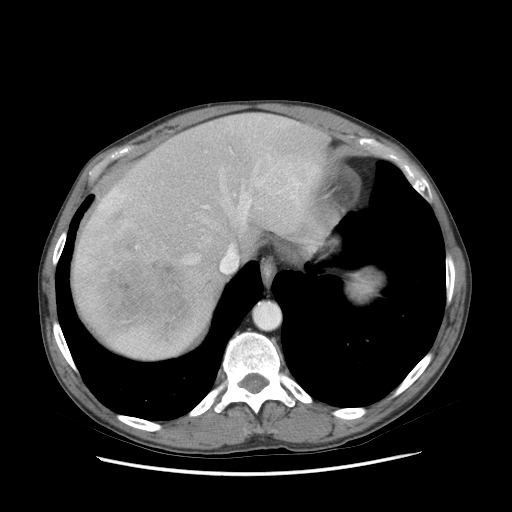
Contrast-enhanced abdominal CT (liver protocol), one axial slice; slice 65 of 89 in the series (ordered by position); reconstruction kernel STANDARD; 140 kVp; soft-tissue window (W 400 / L 40 HU); 2.5 mm slice thickness; 512 × 512 image matrix, field of view 380 × 380 mm. Case-level facts recorded for this patient, not image findings: diagnosis: hepatocellular carcinoma (patient treated with transarterial chemoembolisation; whether this scan precedes or follows treatment is not stated here); TNM stage (as recorded): Stage-IIIB; Child-Pugh class: A; tumour differentiation: moderately differentiated; tumour nodularity: multinodular.
Outlined on this slice (semi-automatically segmented with operator editing):
- abdominal aorta: bounding box (x1, y1, x2, y2) in pixels: (255, 304, 279, 328)
- liver parenchyma outside the tumour (the mass and vessels are separate outlines, so this box may not span the whole liver): (72, 114, 336, 358)
- mass: (87, 207, 200, 337)
- liver vessels: (83, 155, 312, 263)